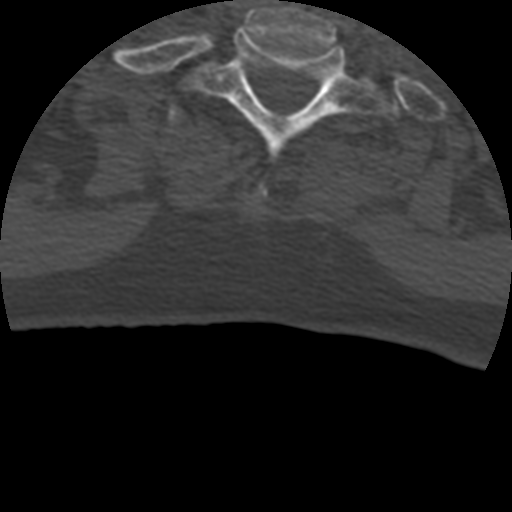
CT including the spine, one axial slice. Slice 385 of 399 in the series (ordered by position). 120 kVp. Bone window (W 1800 / L 400 HU). 512 × 512 image matrix. Patient age 69 years. From the clinical record (not read from this slice): primary cancer: prostate.
Structures marked on this image (semi-automatic segmentation, software-assisted and operator-edited):
- T1 vertebra: bounding box (x1, y1, x2, y2) in pixels: (193, 29, 386, 164)
- T2 vertebra: (168, 101, 186, 129)